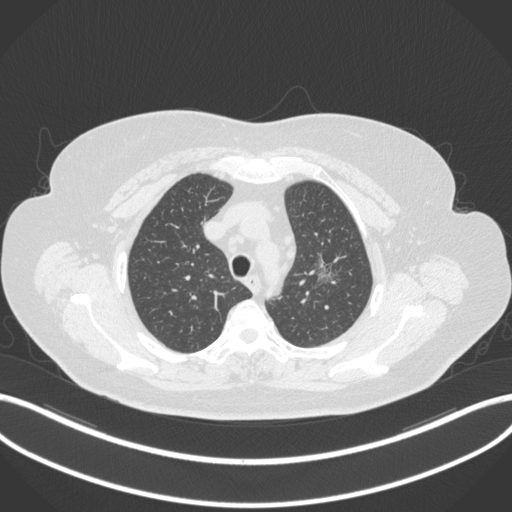
Chest CT, one axial slice; slice 265 of 310 in the series (ordered by position); reconstruction kernel B31f; lung window (W 1500 / L -600 HU); 1 mm slice thickness; 512 × 512 image matrix, field of view 400 × 400 mm. Female patient, age 70 years. From the clinical record (not read from this slice): clinical TNM (as recorded): T1c N0 M0.
Structures marked on this image (bounding box drawn by a radiologist):
- lung tumour (recorded histology: adenocarcinoma): box from (x=309, y=250) to (x=344, y=286) px